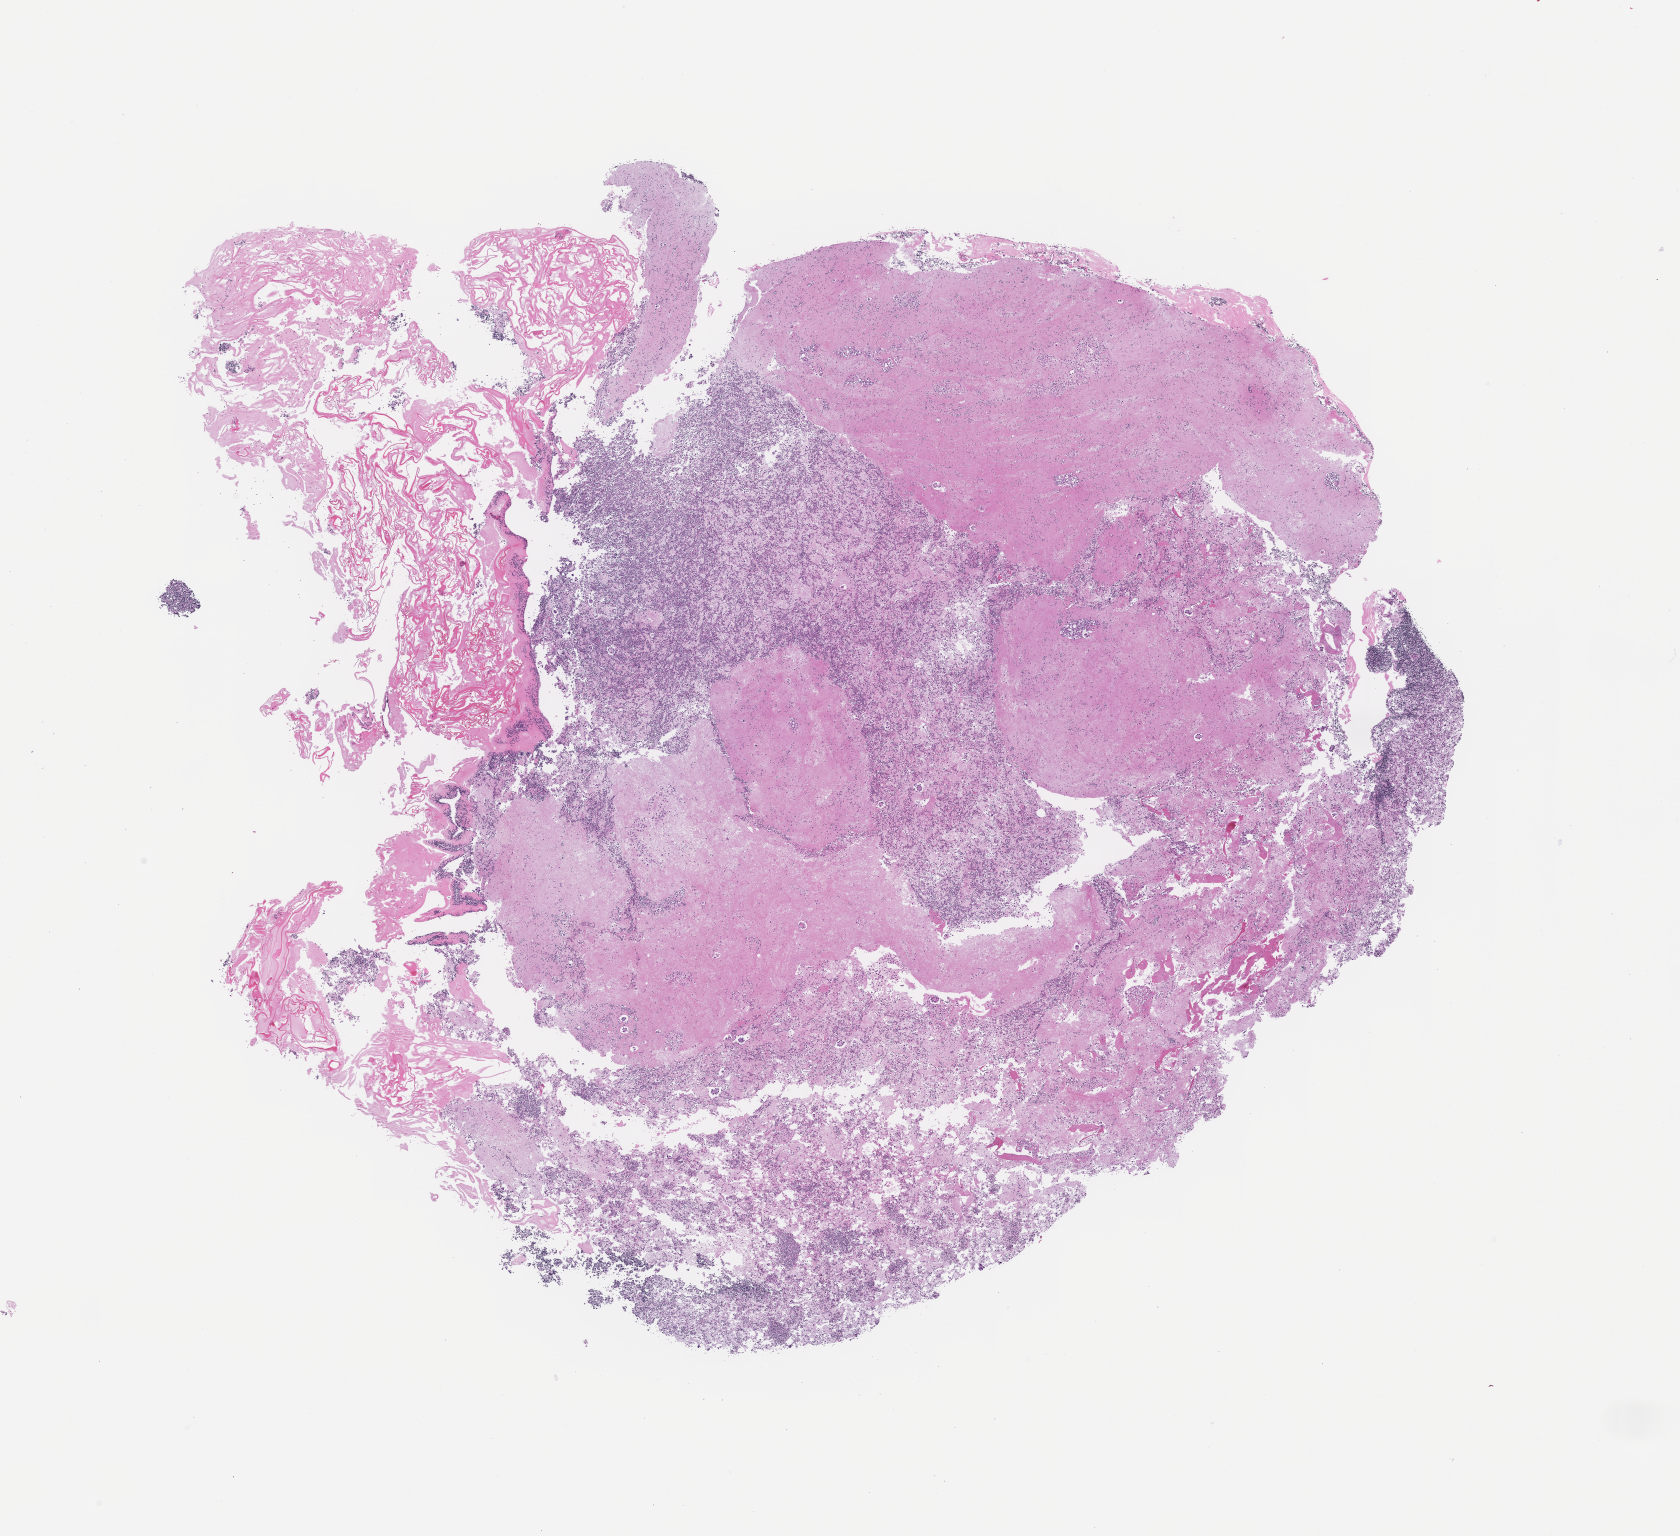
Digitized H&E-stained section, low-resolution overview of the scanned area, about 13.6 x 12.4 mm; formalin-fixed paraffin-embedded section; site: lung; archival tissue. Patient sex: female.
This section: primary tumor. Diagnosis: Non-Small Cell Lung Carcinoma.